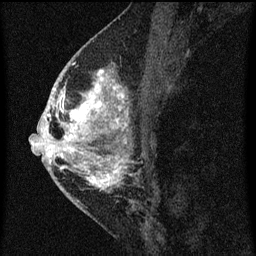
Breast MRI (dynamic contrast-enhanced), one sagittal slice. Position 31 of 60 along the scan axis. Dynamic contrast-enhanced series, image 2 of 3 at this slice position (ordered by acquisition). 1.5 T. TE 4.2 ms, TR 8 ms. 2 mm slice thickness. 256 × 256 image matrix, field of view 180 × 180 mm. Patient: female, 46 years.
Outlined on this slice (semi-automatic segmentation, software-assisted and operator-edited):
- analysis volume of interest (the breast-tissue region the enhancement analysis was run in; not a lesion): box from (x=48, y=68) to (x=130, y=195) px
- tumour enhancement mask (voxels above the 70 % enhancement threshold inside the analysis volume of interest): (x=48, y=68)–(x=129, y=191)